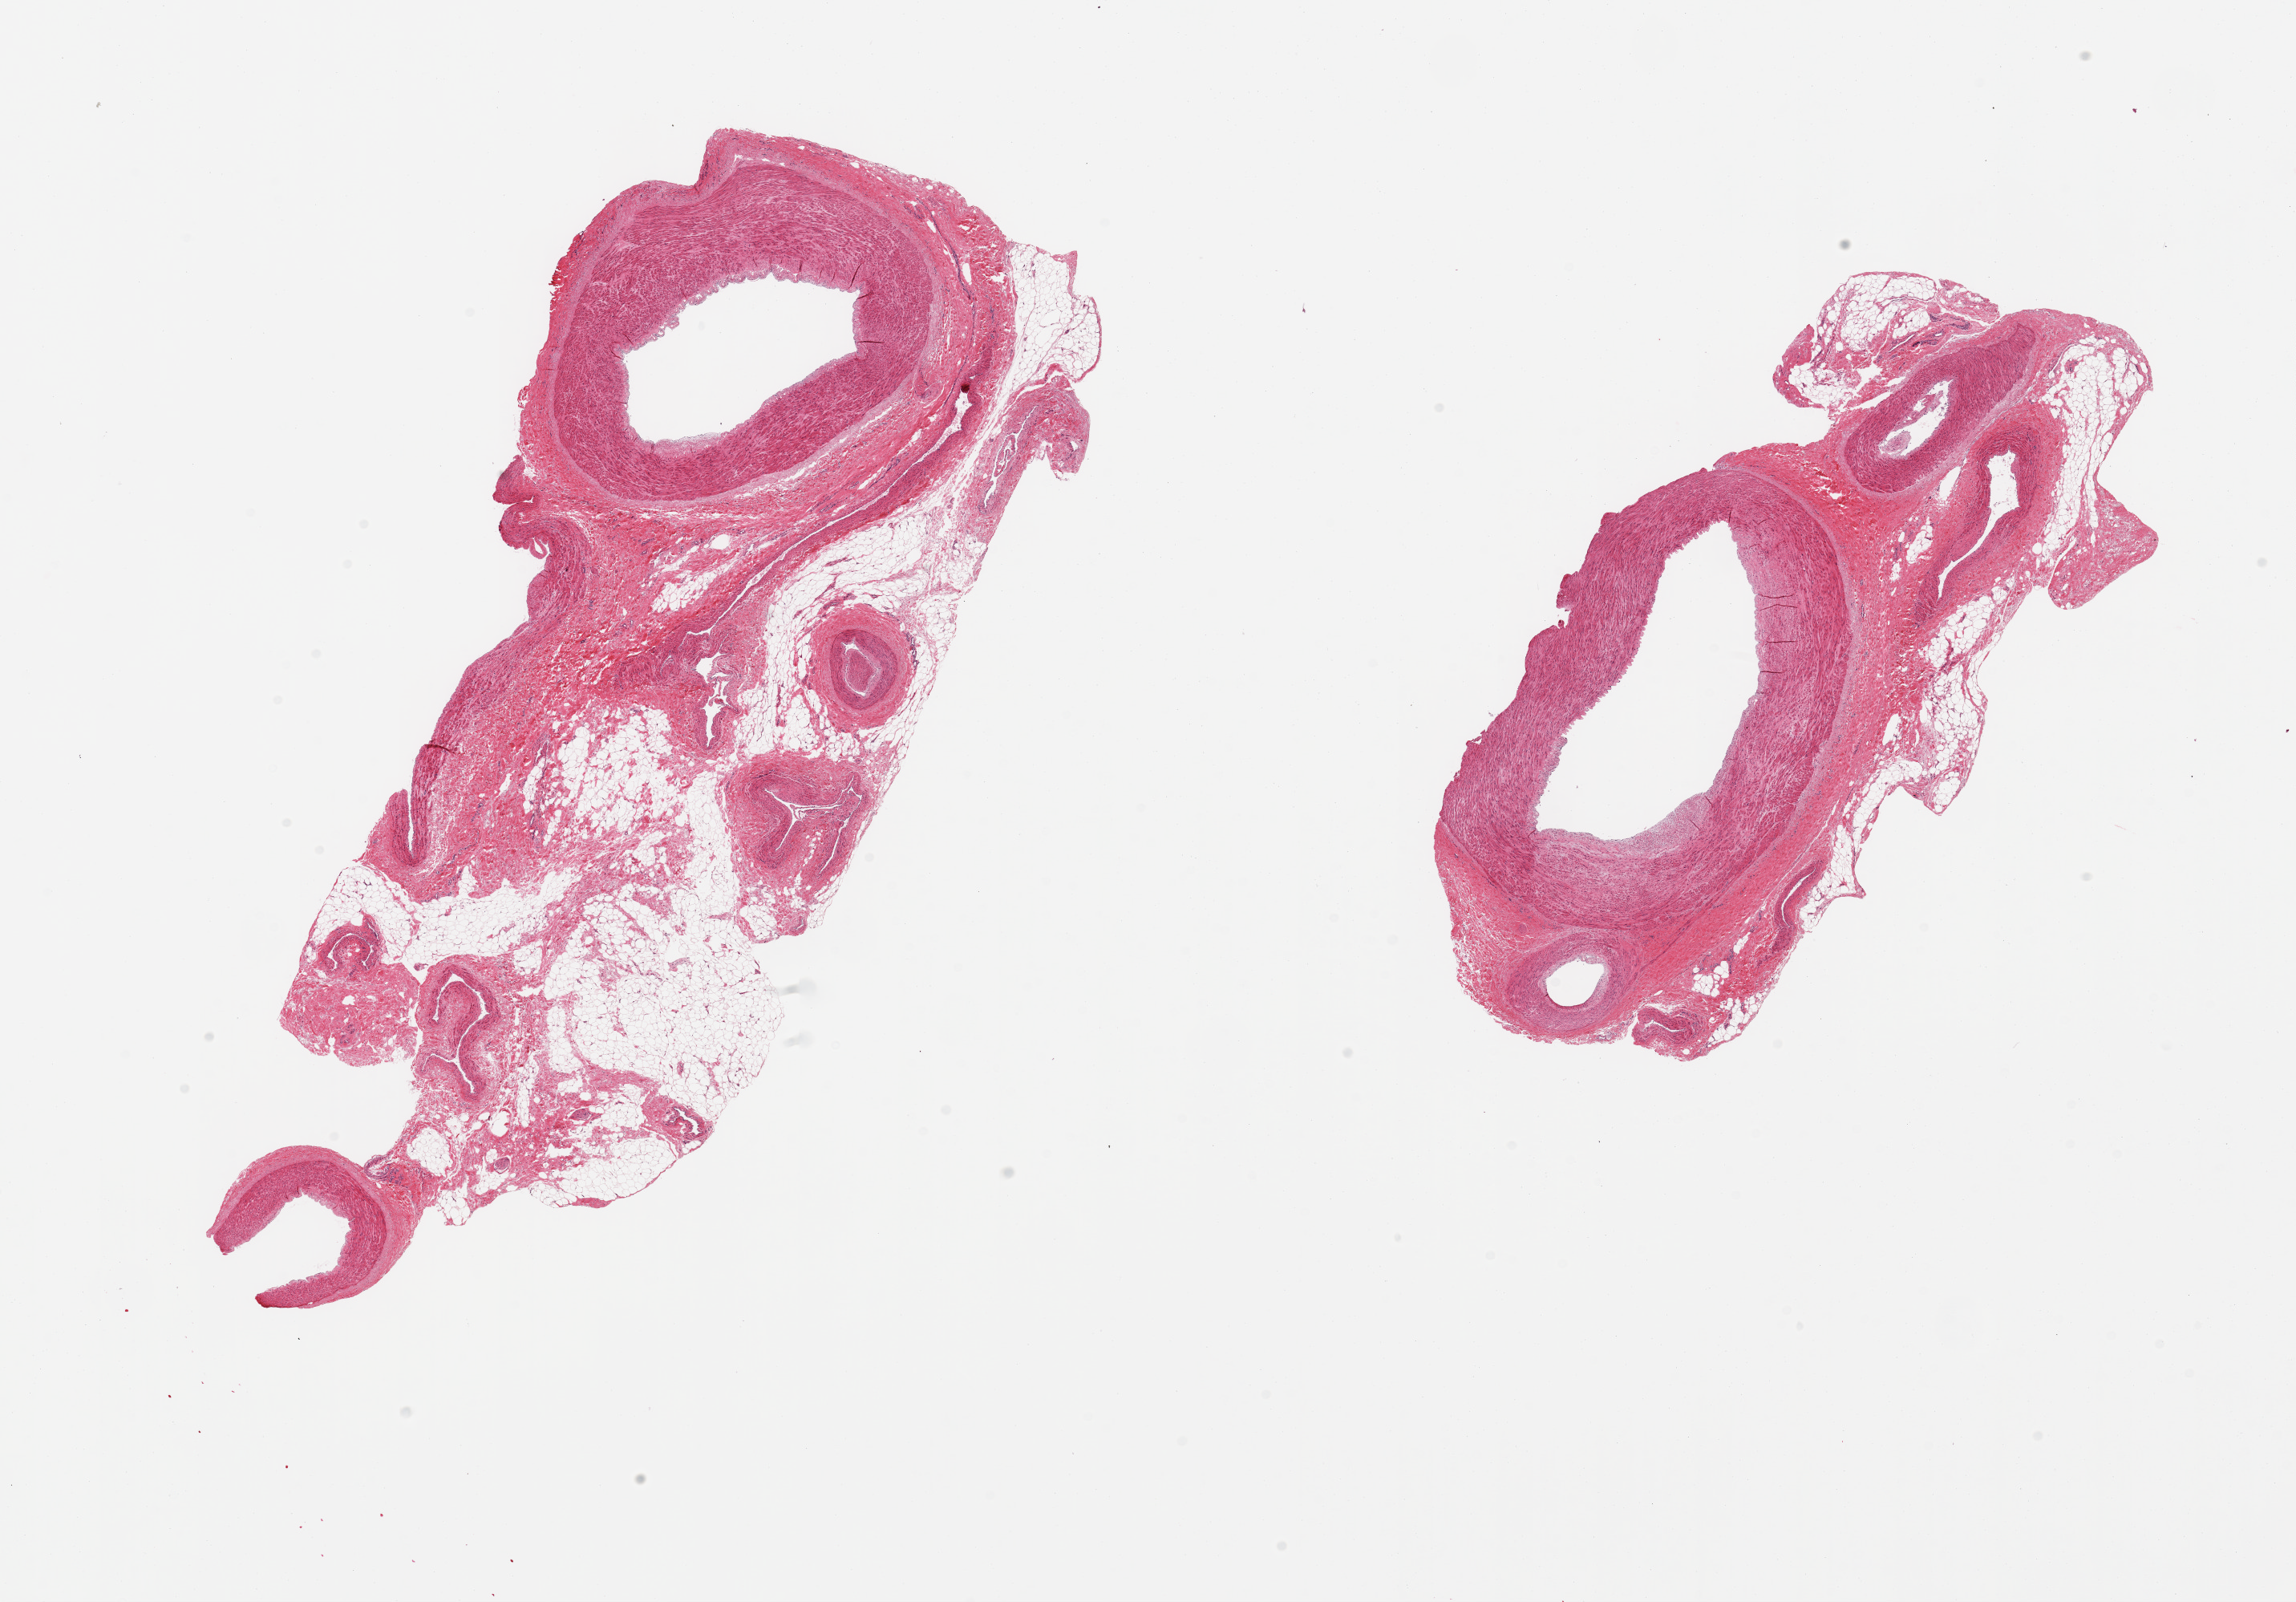
Whole-slide image, H&E stain — a low-resolution overview of the entire scanned area, about 22.6 x 15.8 mm (from a 20x scan), PAXgene-fixed paraffin-embedded (PFPE) section, section of tibial artery (target tissue), donor tissue sample. Donor sex: female.
* pathologist's review note for this sample: 2 pieces;external fat comprises 60% & 20%